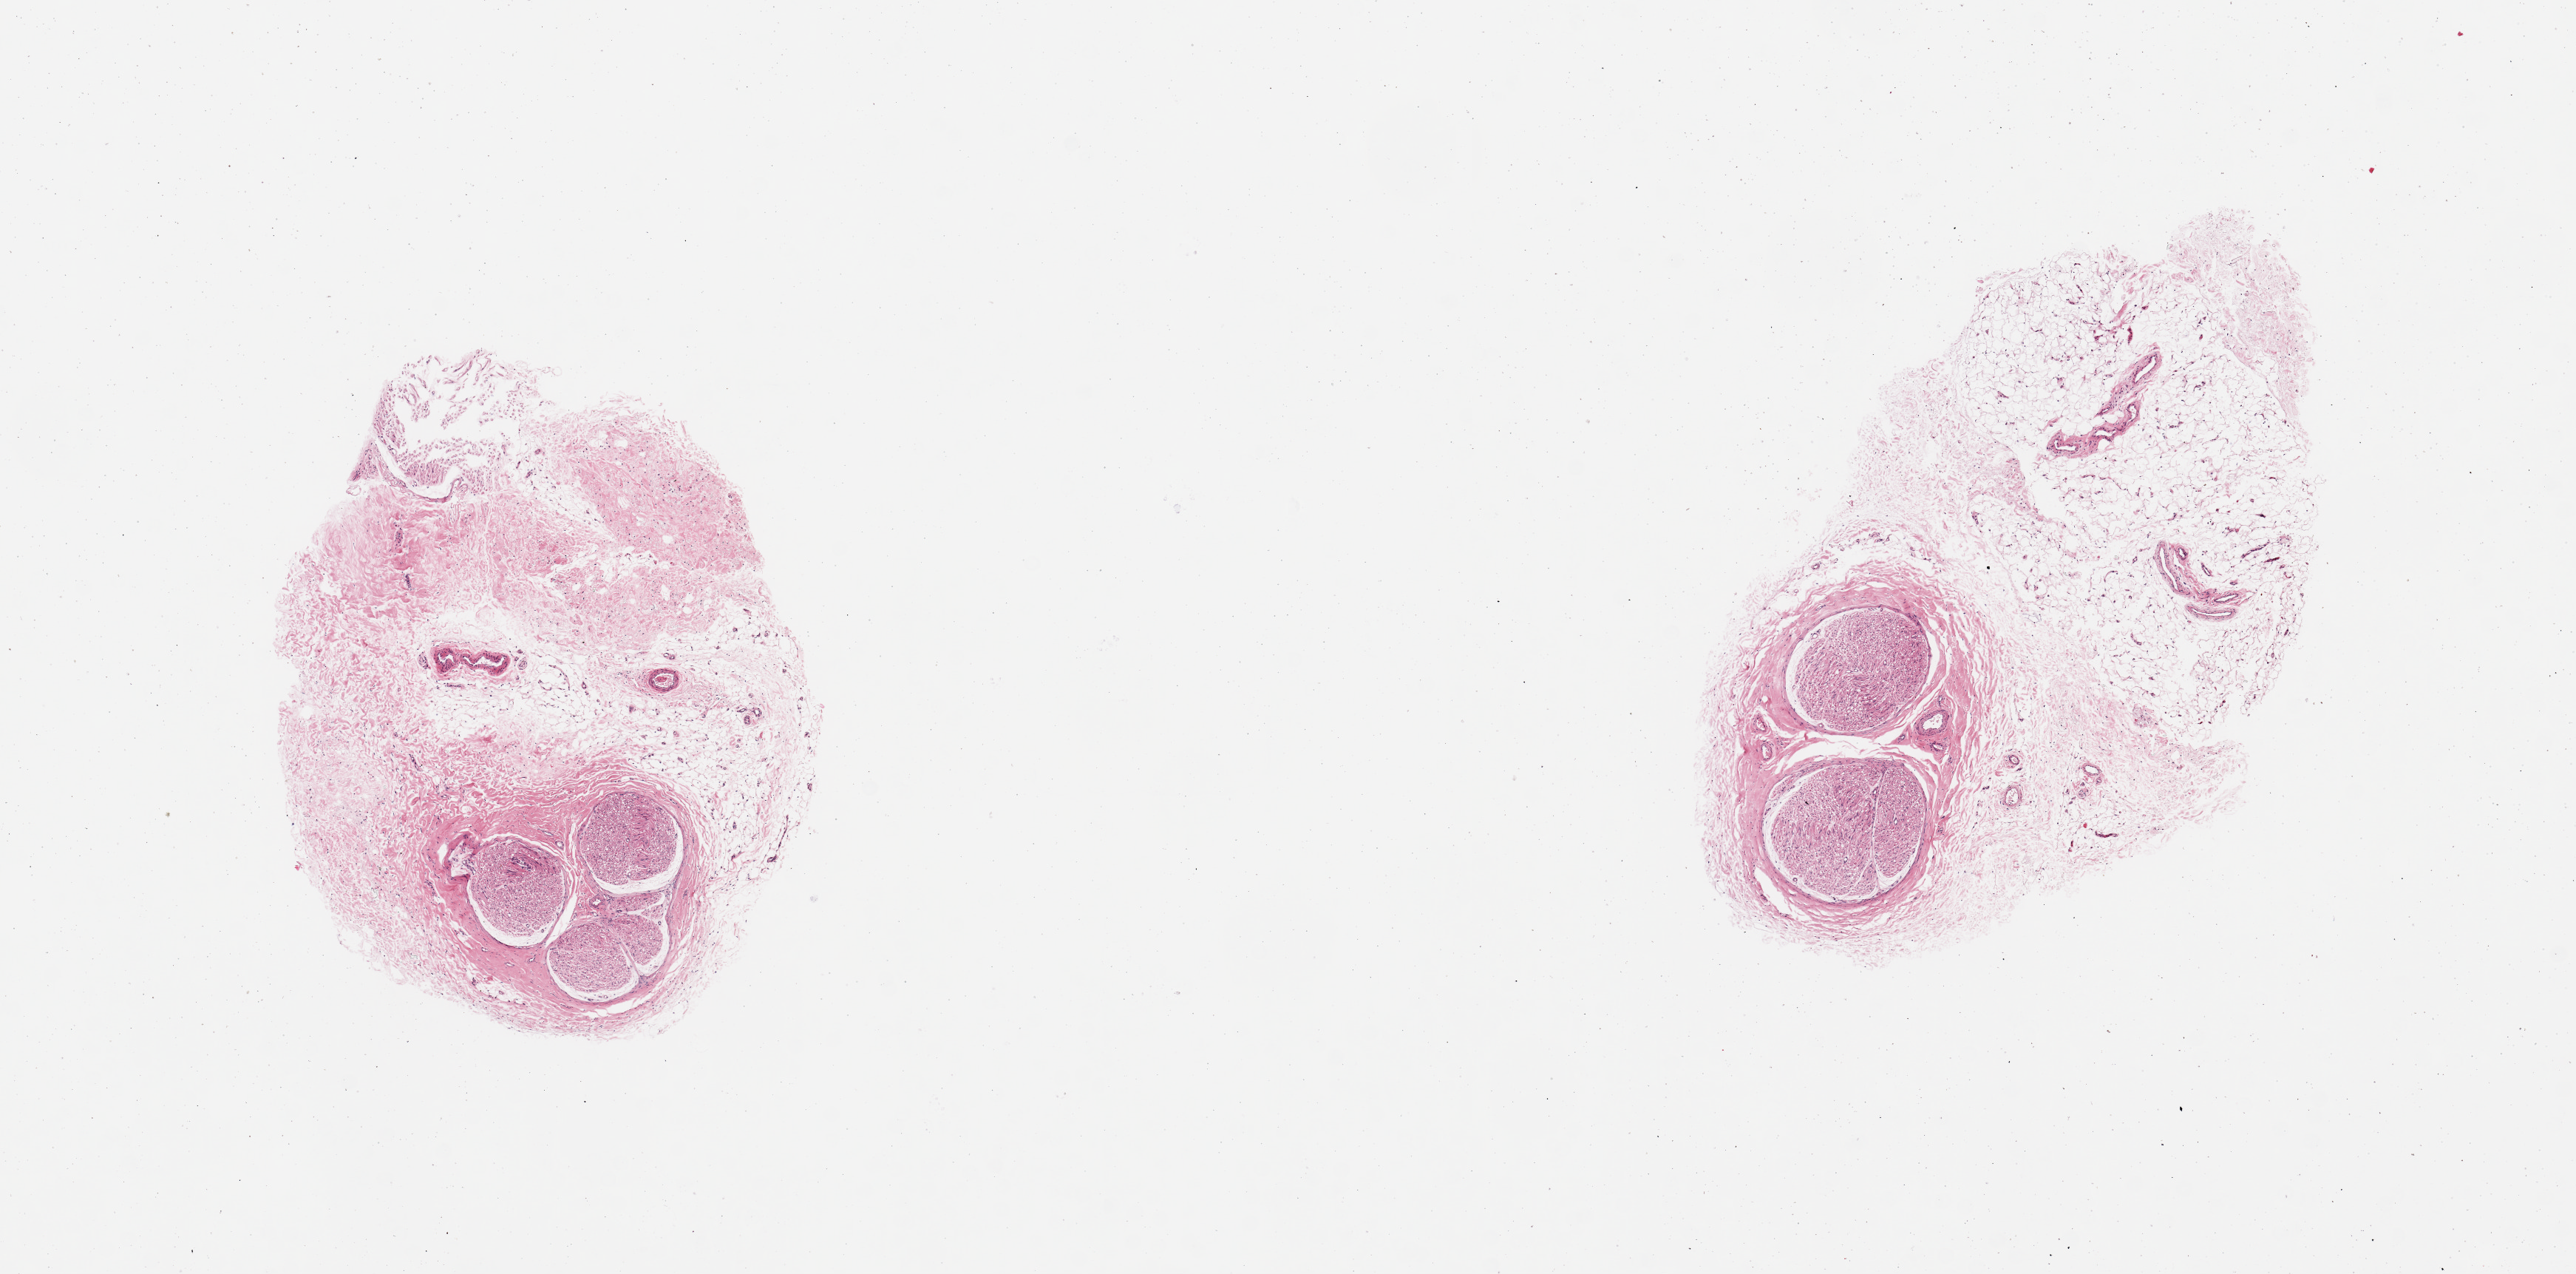
Haematoxylin and eosin whole-slide image — shown as a low-resolution overview of the whole scanned area (about 13.8 x 6.8 mm, acquisition: 20x scan), PAXgene-fixed paraffin-embedded (PFPE) section, target tissue: tibial nerve, donor tissue sample. Donor sex: male.
Reviewer comment on this tissue sample: 2 pieces; 70% external fat.